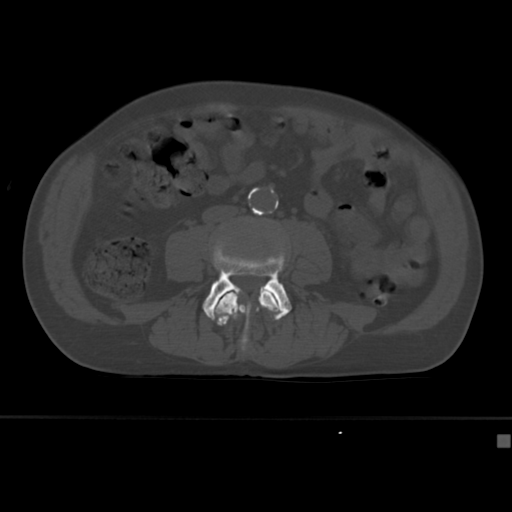
CT including the spine, one axial slice; slice 114 of 430 in the series (ordered by position); reconstruction kernel Br40s; 120 kVp; bone window (W 1800 / L 400 HU); 1.5 mm slice thickness; 512 × 512 image matrix. Male patient, age 64 years. From the clinical record (not read from this slice): primary cancer: uterus.
Outlined on this slice (semi-automatic segmentation, software-assisted and operator-edited):
- L3 vertebra: bounding box <215,292,281,354> (left, top, right, bottom; pixels)
- L4 vertebra: <202,238,292,352>